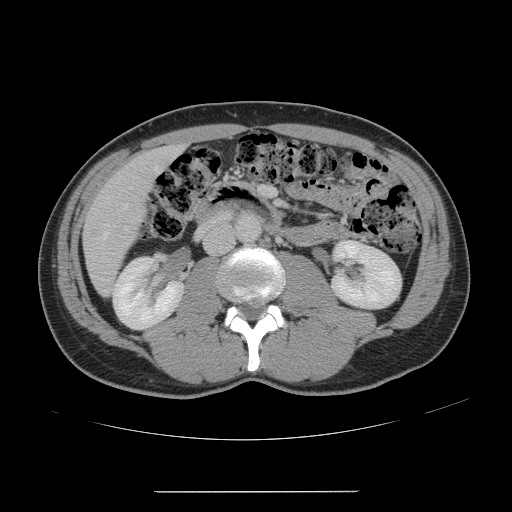
Contrast-enhanced abdominal CT, one axial slice. 120 kVp. Intravenous contrast given. Soft-tissue window (W 400 / L 40 HU). 2.5 mm slice thickness. 512 × 512 image matrix, field of view 401 × 401 mm. Male patient, age 53 years. Case-level facts recorded for this patient, not image findings: diagnosis: colorectal cancer liver metastases, imaged before liver resection.
Outlined on this slice (expert manual segmentation):
- hepatic veins: bounding box (x1, y1, x2, y2) in pixels: (100, 167, 160, 241)
- liver: (84, 148, 179, 295)
- portal vein (with intrahepatic branches): (260, 187, 267, 195)